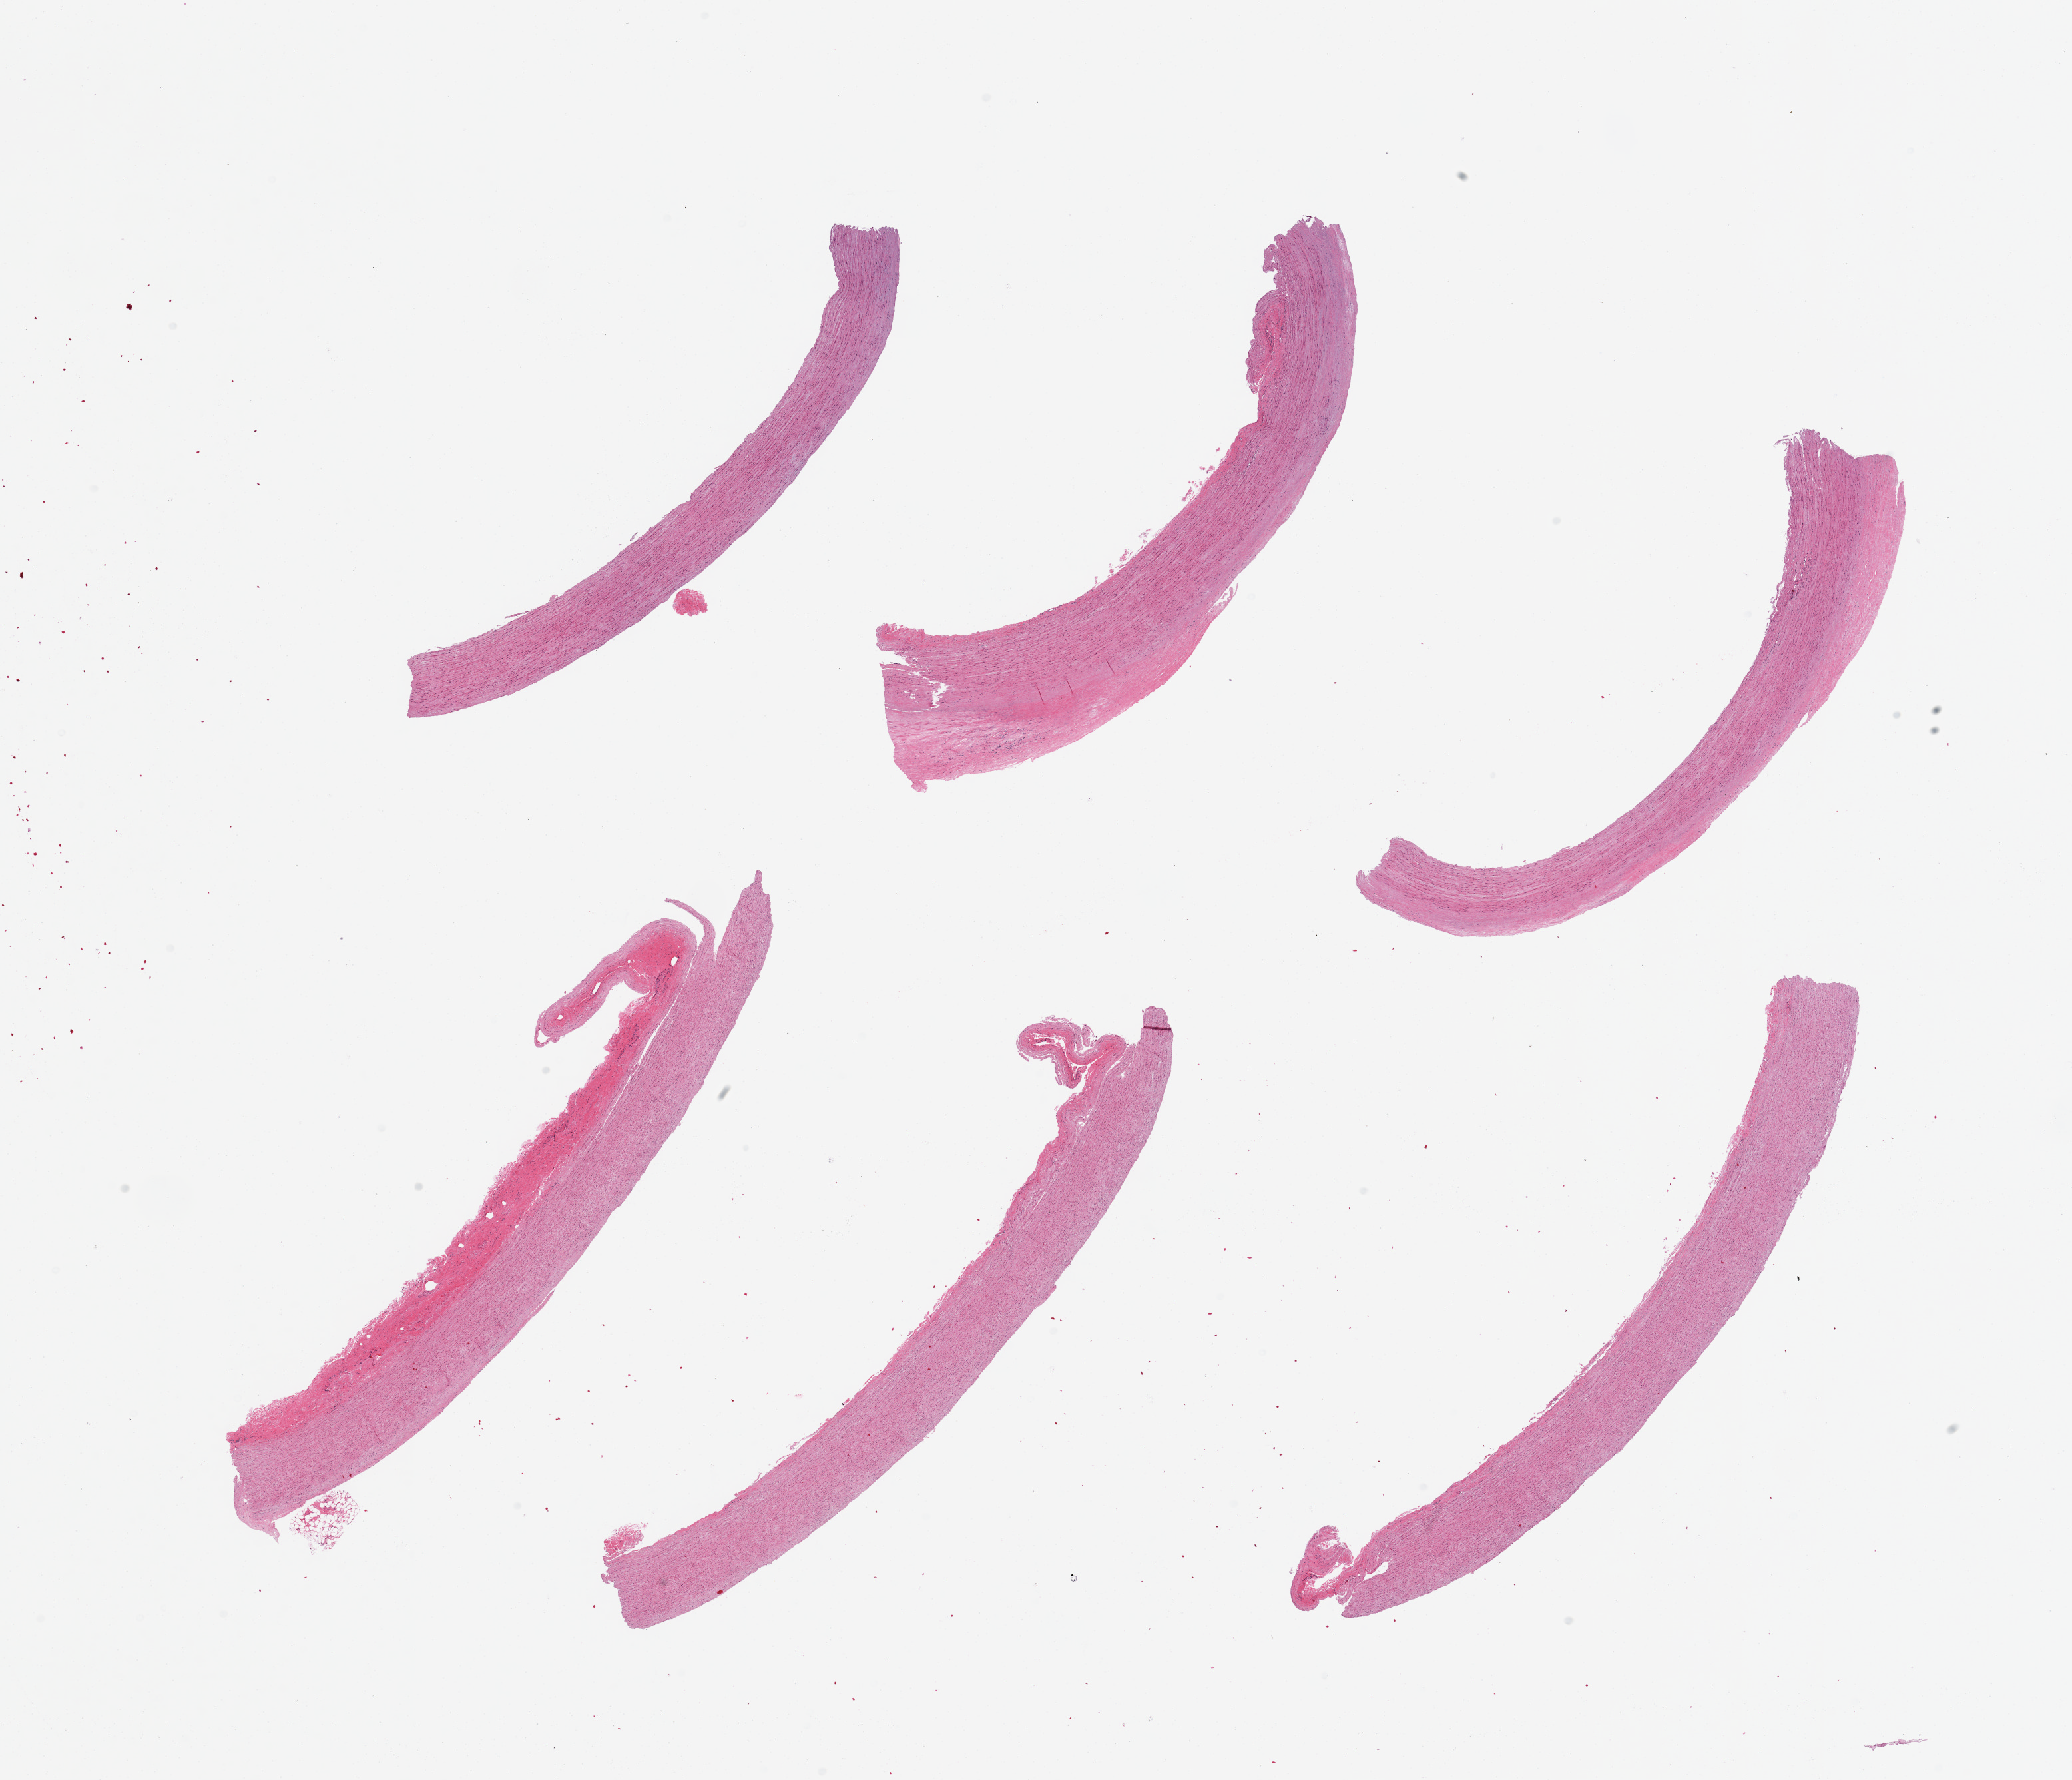
Digitized haematoxylin and eosin-stained section — low-resolution overview of the scanned area, about 24.6 x 21.1 mm. PAXgene-fixed, paraffin-embedded tissue. Sampled site (target tissue): aorta. Donor tissue sample.
- review note (as recorded): 6 pieces; up to 1mm thick atherosclerotic plaque